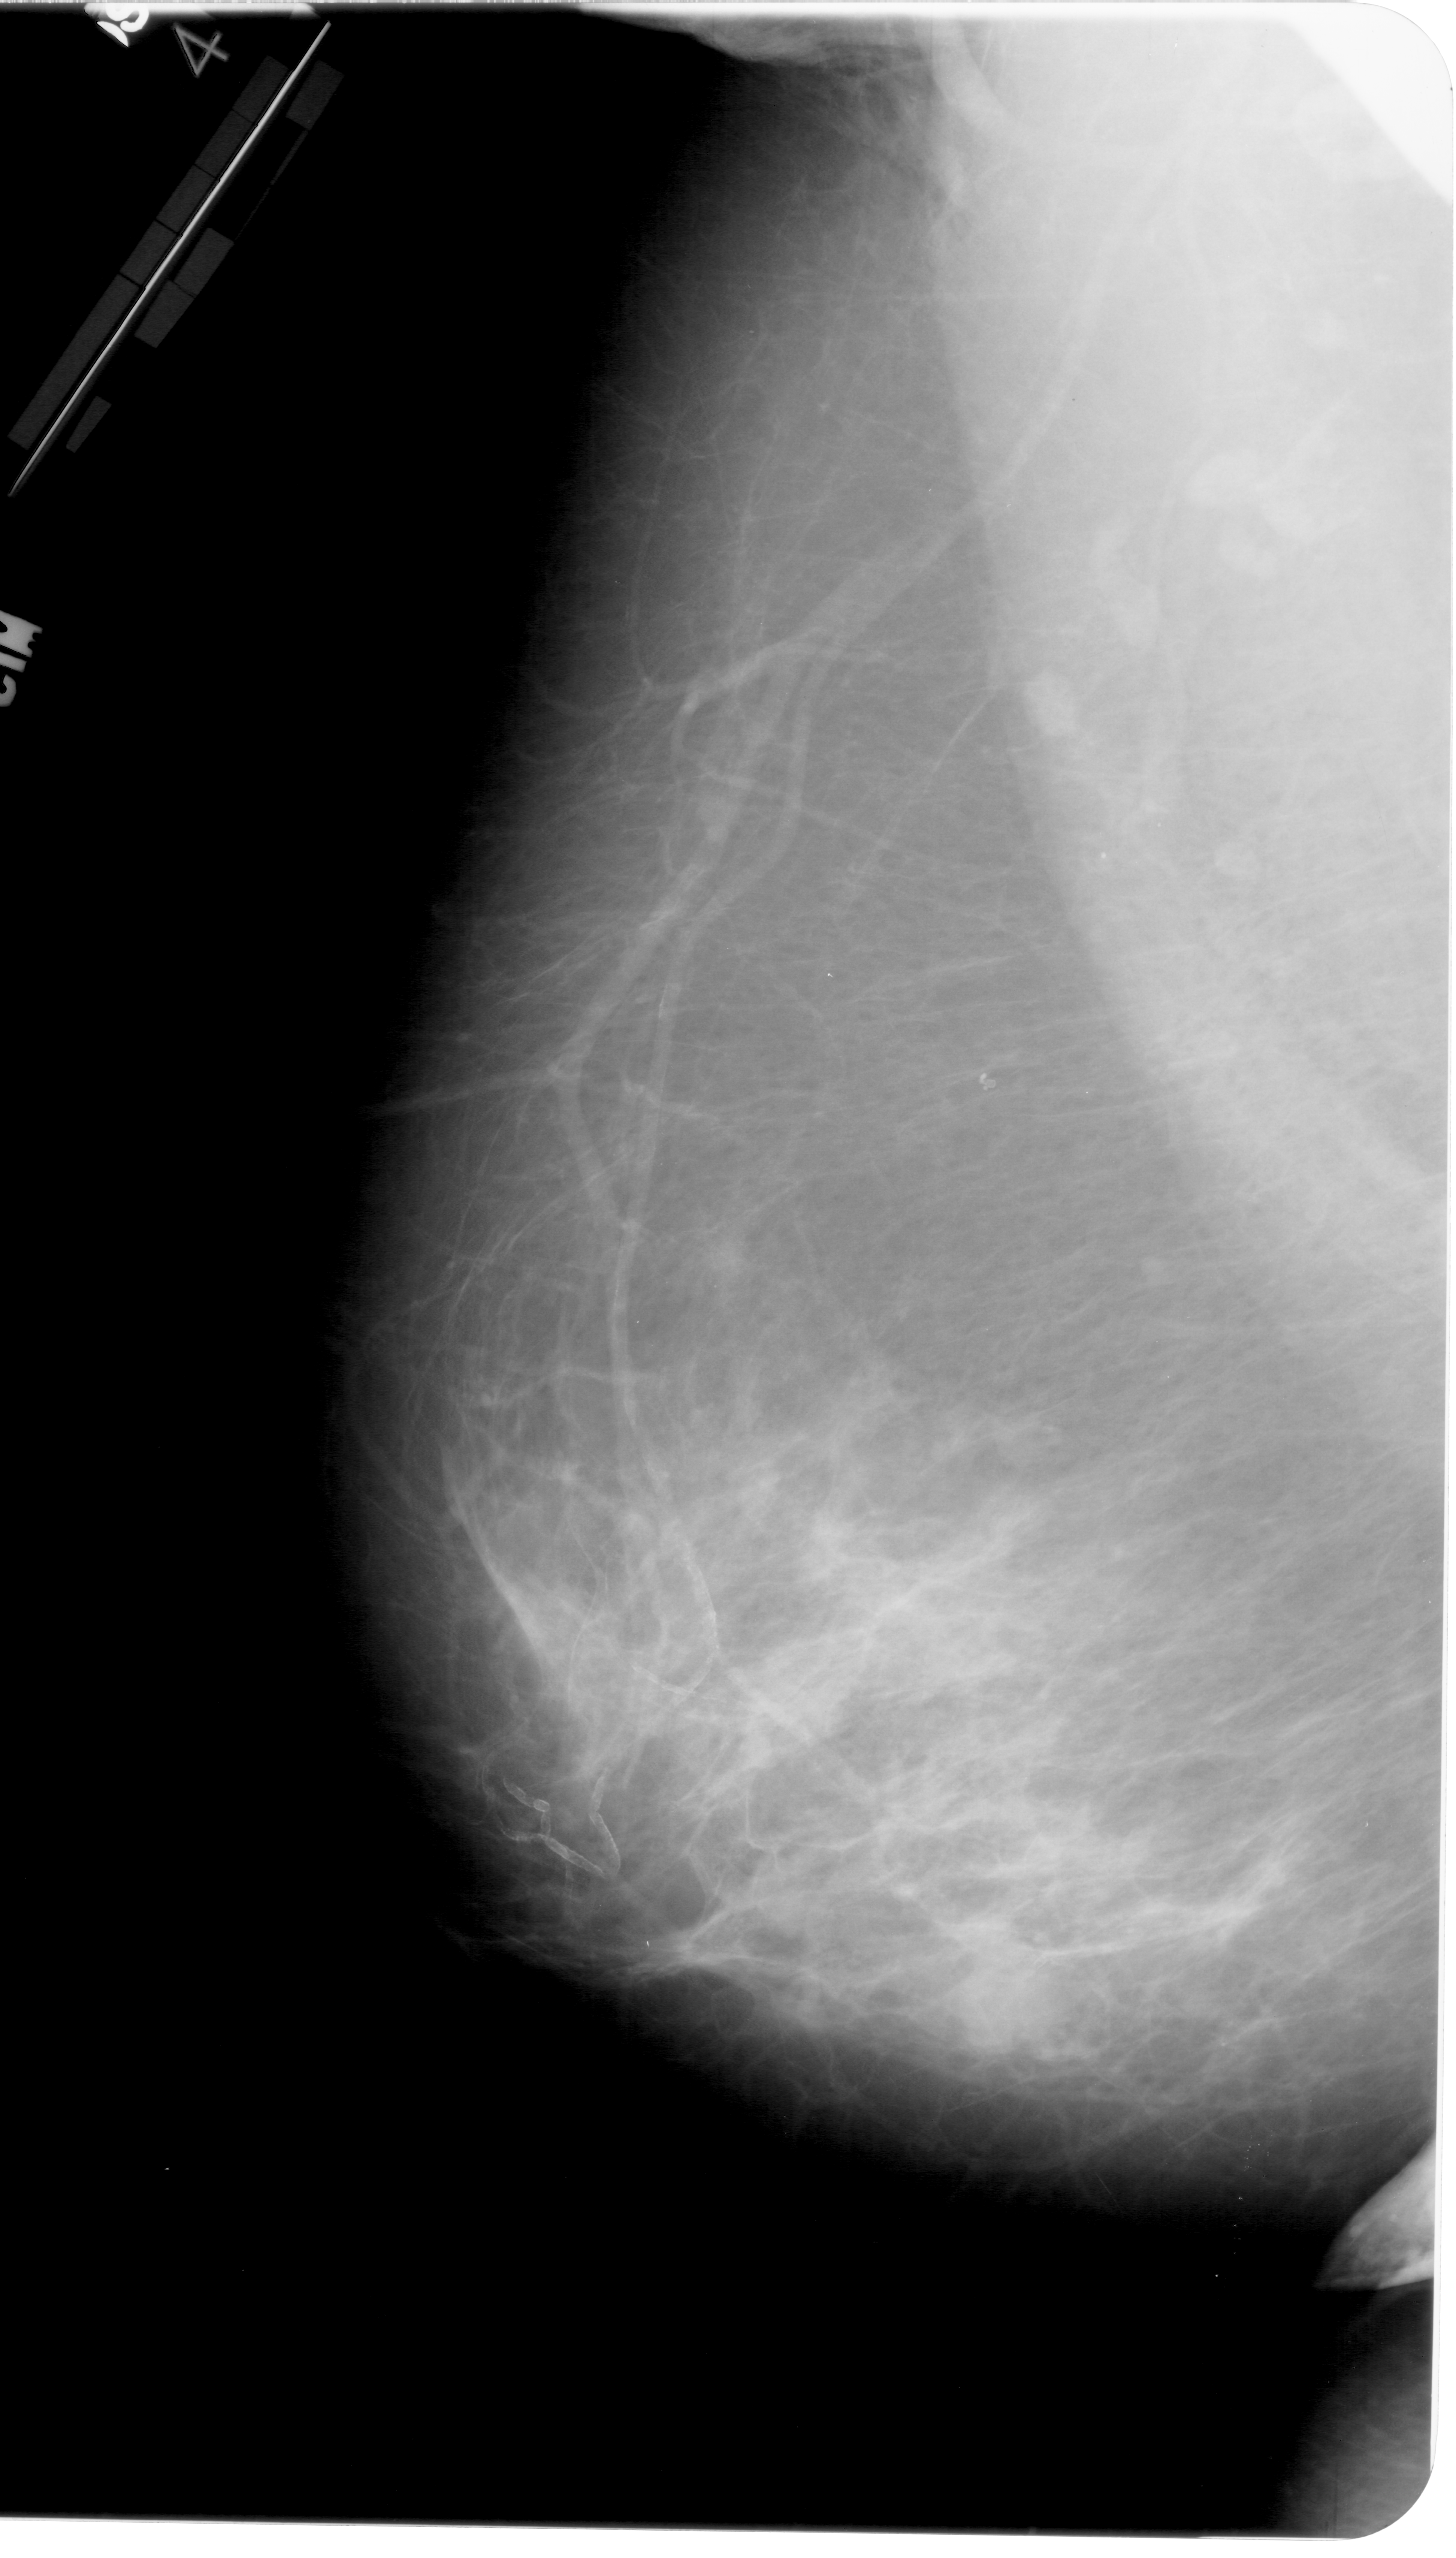
Scanned film-screen mammogram. Left breast. Mediolateral oblique (MLO) view. Breast composition: heterogeneously dense (BI-RADS density category 3 of 4). 1456 × 2558 image matrix.
Marked abnormalities (boxes around the expert regions of interest):
- mass, shape round, margins ill defined; BI-RADS assessment category 4; subtlety rating 3 on a 1 (subtle) to 5 (obvious) scale; pathology (as recorded): malignant: bounding box [x1, y1, x2, y2] px = [923, 1928, 1076, 2056]